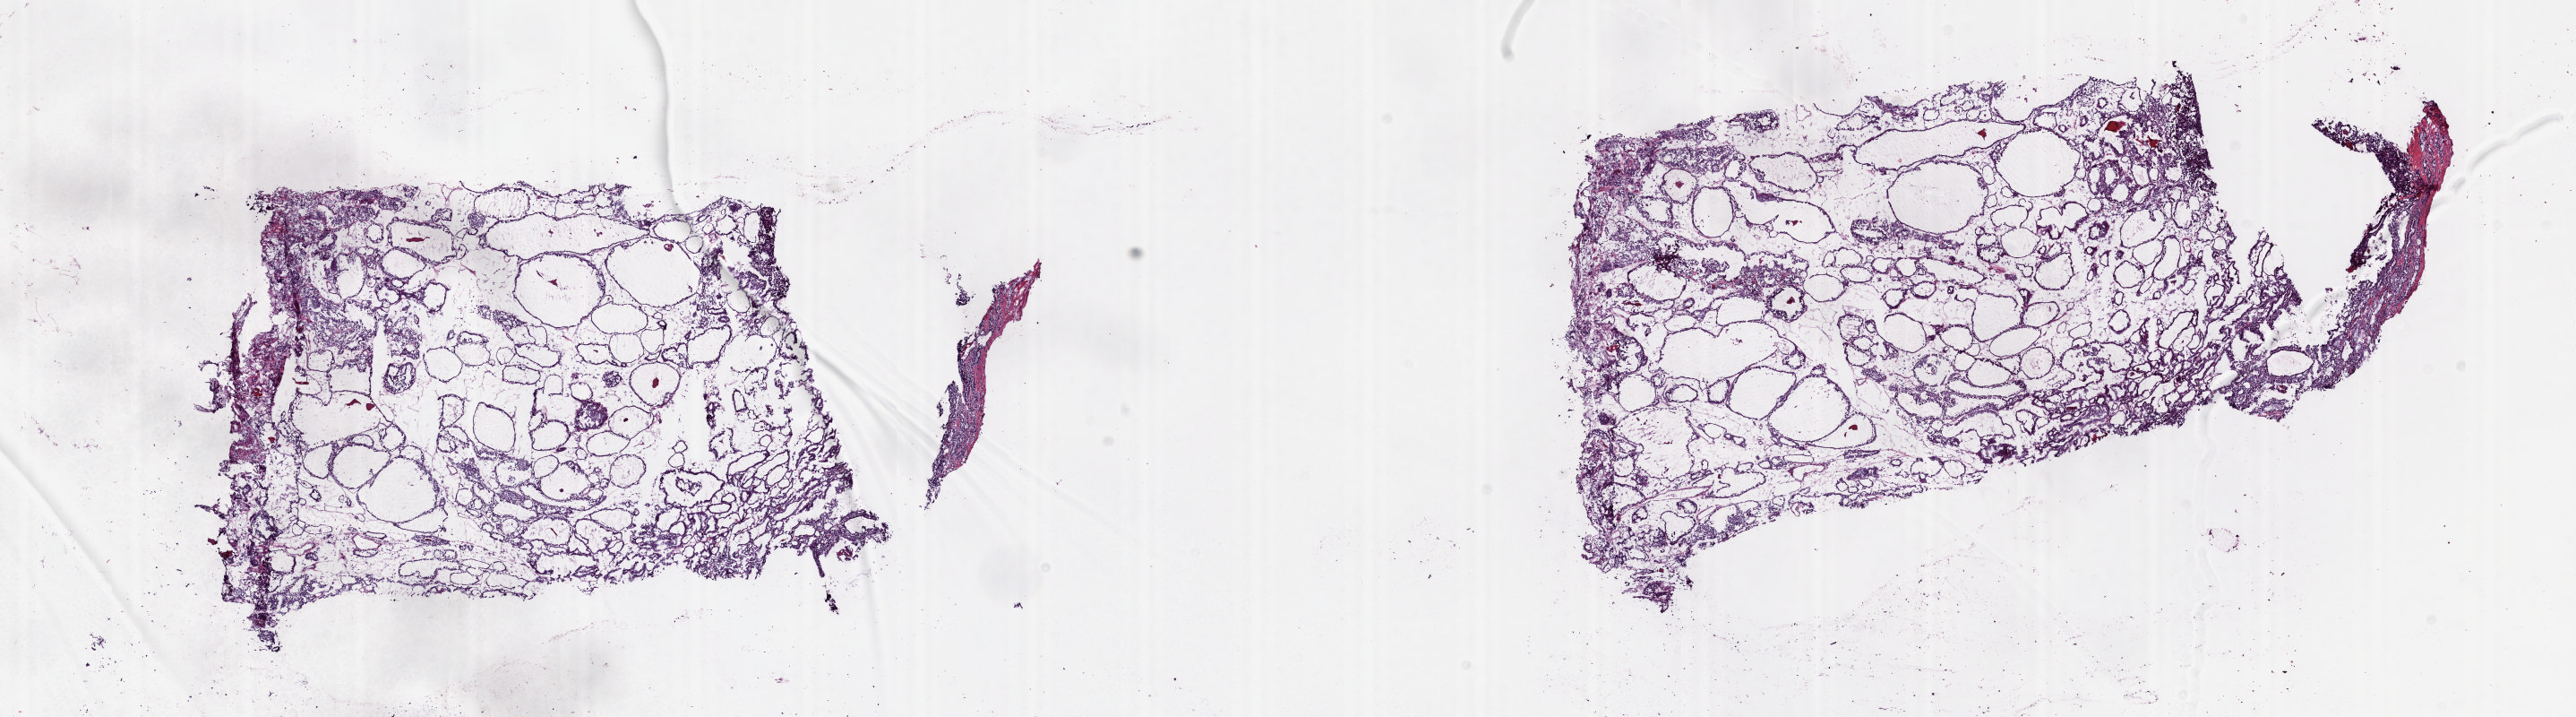
Digitized Hematoxylin and eosin (H&E) stained tissue section (whole slide), whole scanned area (about 22.8 x 6.3 mm, acquisition: 20x scan) shown as a low-resolution overview, frozen section from the top of the tissue portion, thyroid, solid tissue normal (non-tumour tissue) sample. Female, age 32 years at initial diagnosis. Composition of this section per pathologist review: tumour cells 0%, tumour nuclei 0%, normal cells 90%, stromal cells 10%, necrosis 0%. Inflammatory infiltration, as recorded: lymphocyte infiltration 3%, monocyte infiltration 0%, neutrophil infiltration 0%.
• this section: solid tissue normal (non-tumour) sample from the same patient
• patient diagnosis: Papillary adenocarcinoma, NOS (thyroid gland)